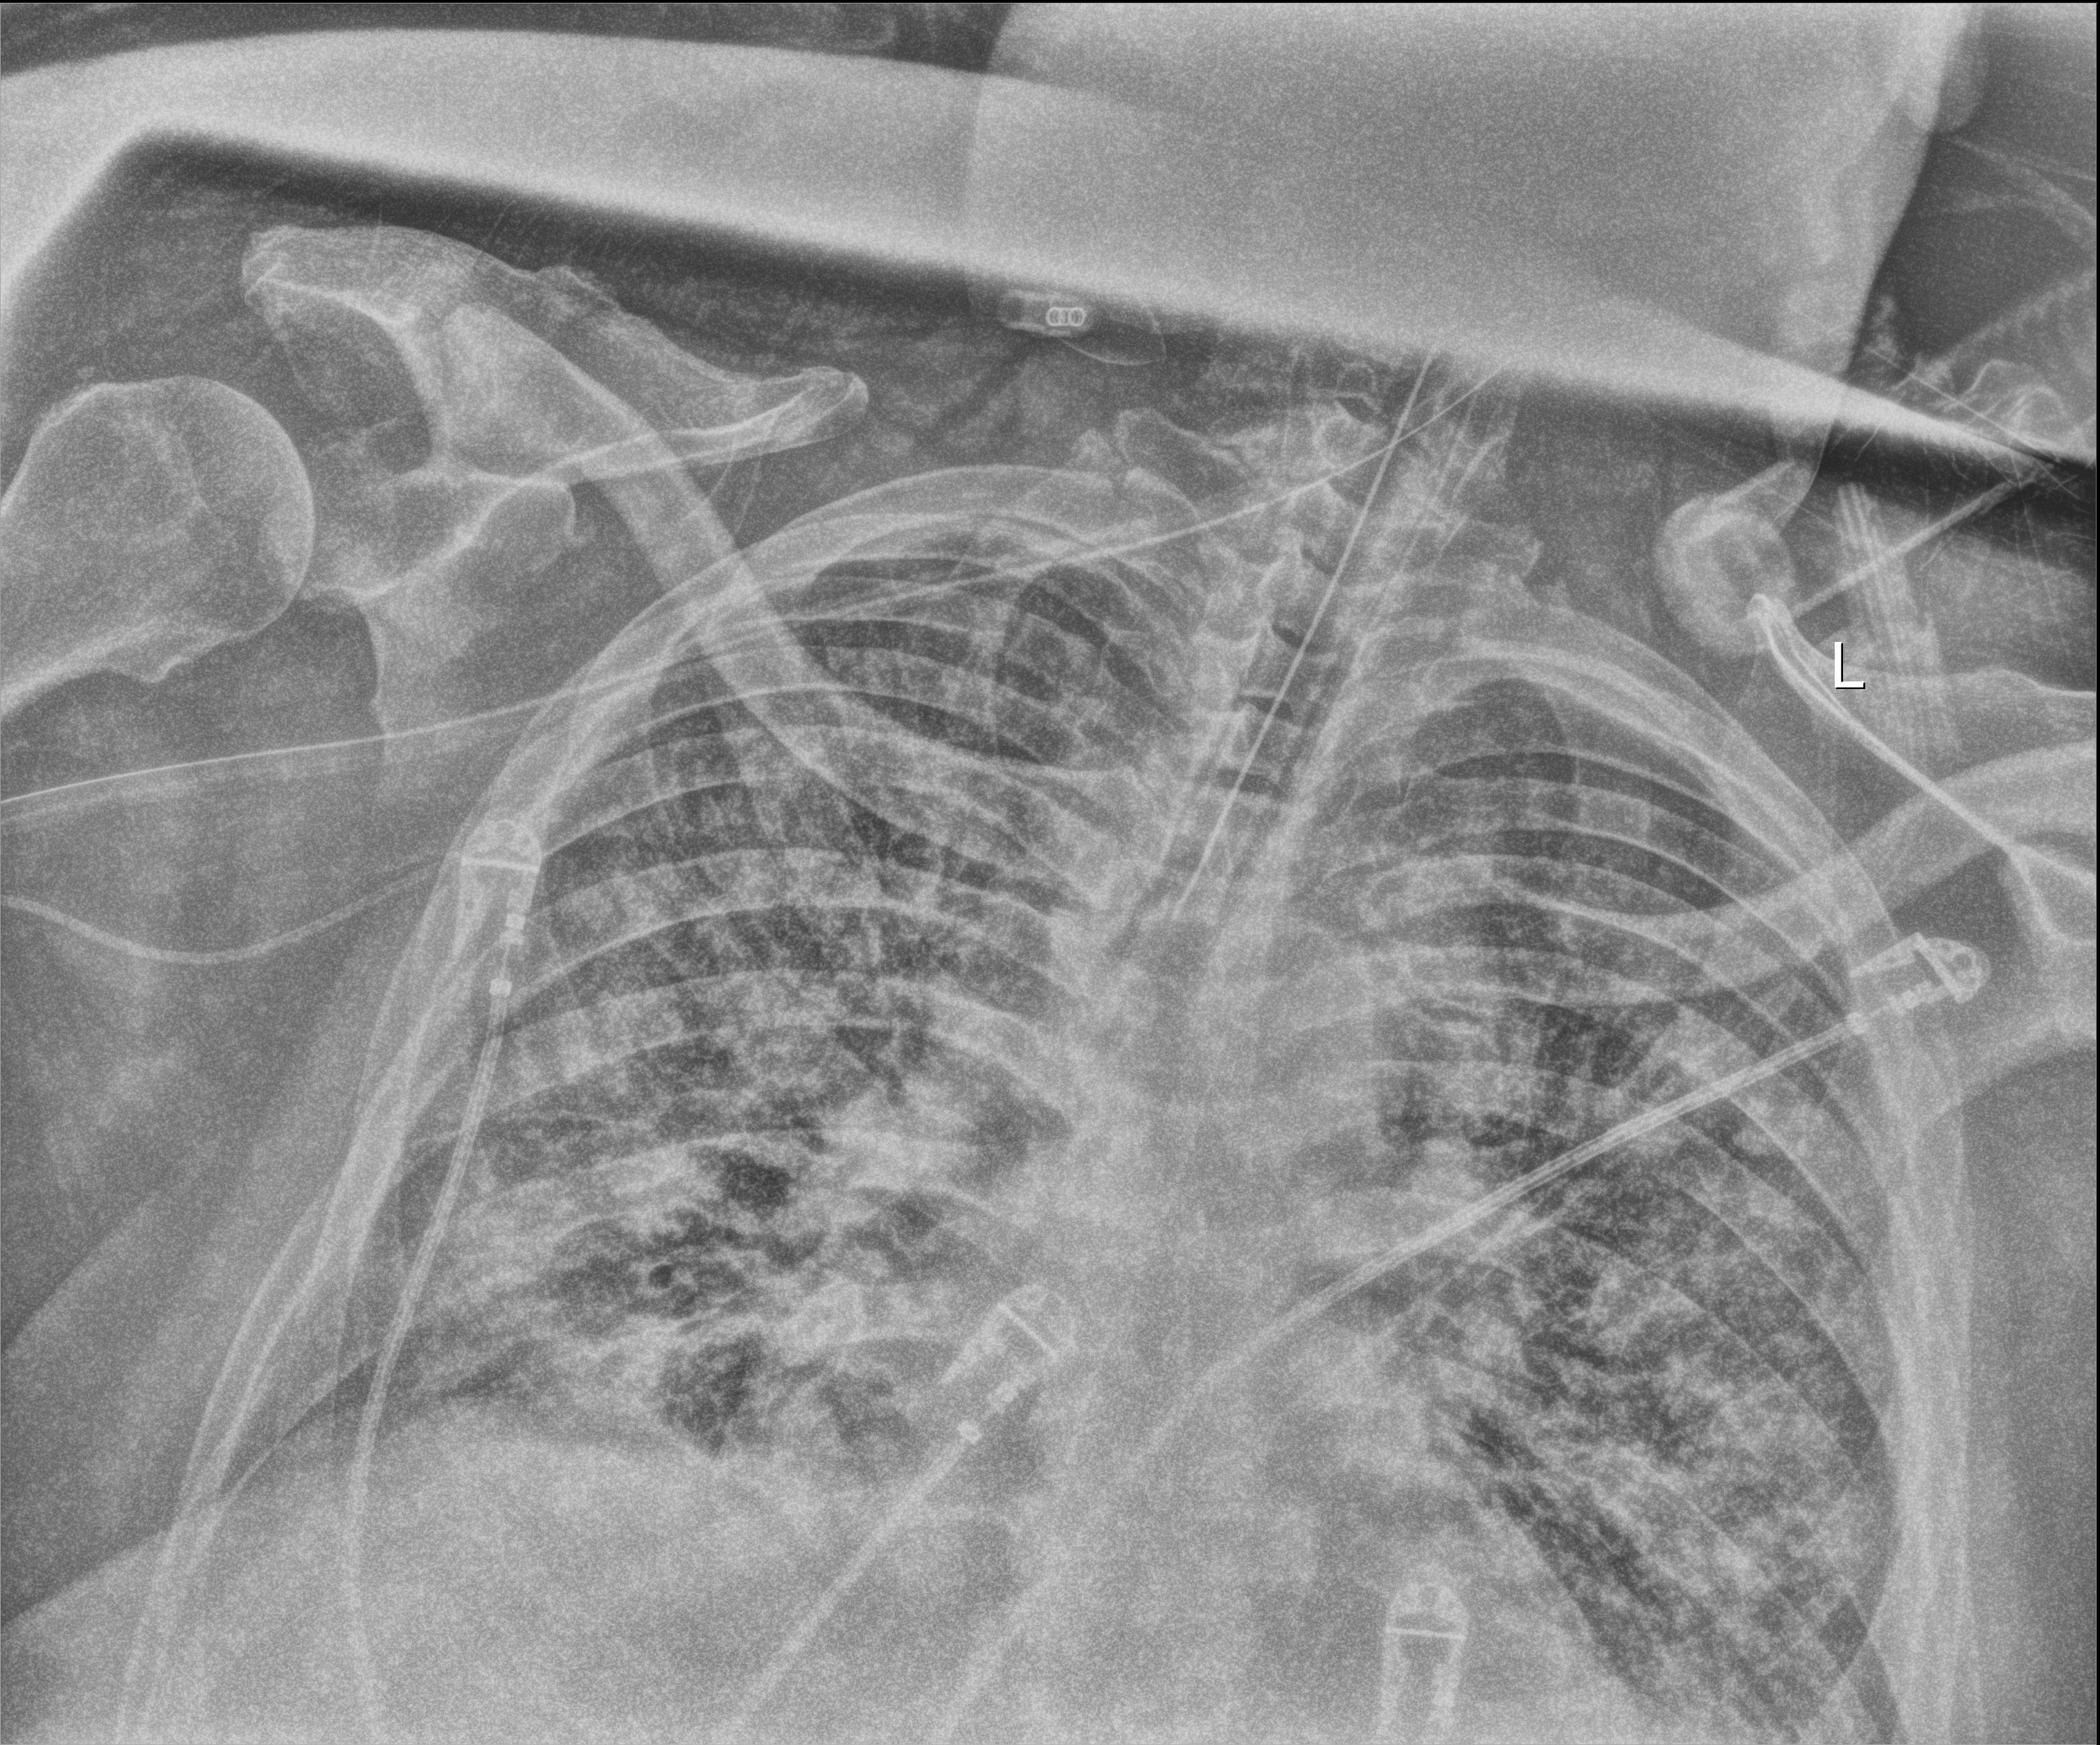
Chest X-ray (portable). Male patient hospitalised with COVID-19, age 60–74 years.
From the hospital-stay record, not from the radiograph (when in the stay this image was taken is not recorded):
- smoking status (admission record): never